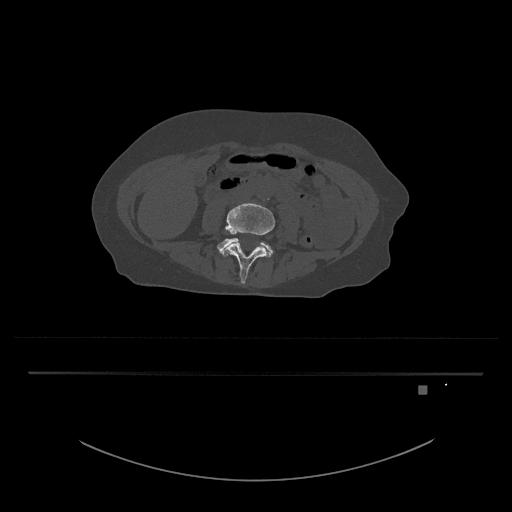
CT including the spine, one axial slice. Slice 348 of 797 in the series (ordered by position). Reconstruction kernel Br40s/3. 120 kVp. Bone window (W 1800 / L 400 HU). 0.5 mm slice thickness. 512 × 512 image matrix, field of view 500 × 500 mm. Patient: female, 57 years. From the clinical record (not read from this slice): primary cancer: cervical.
Structures marked on this image (semi-automatic segmentation, software-assisted and operator-edited):
- L4 vertebra: bounding box [x1, y1, x2, y2] px = [220, 203, 275, 284]